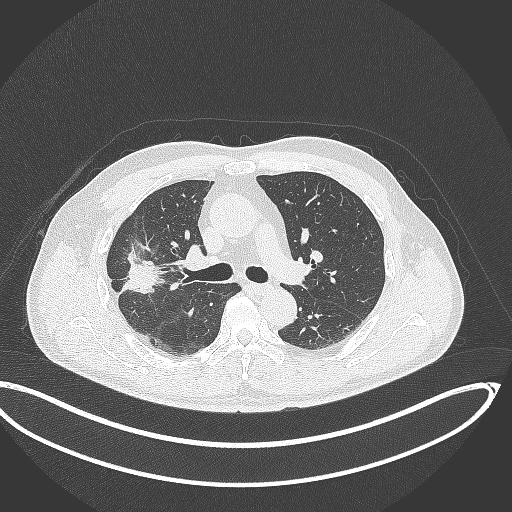
Chest CT, one axial slice; slice 215 of 391 in the series (ordered by position); reconstruction kernel B70f; 120 kVp; lung window (W 1500 / L -600 HU); 512 × 512 image matrix. Patient: male, 63 years. From the clinical record (not read from this slice): clinical TNM (as recorded): T1c N0 M0.
Annotated regions visible in this slice (rectangle marked by the reading radiologist):
- lung tumour (recorded histology: adenocarcinoma): box from (x=118, y=244) to (x=162, y=297) px